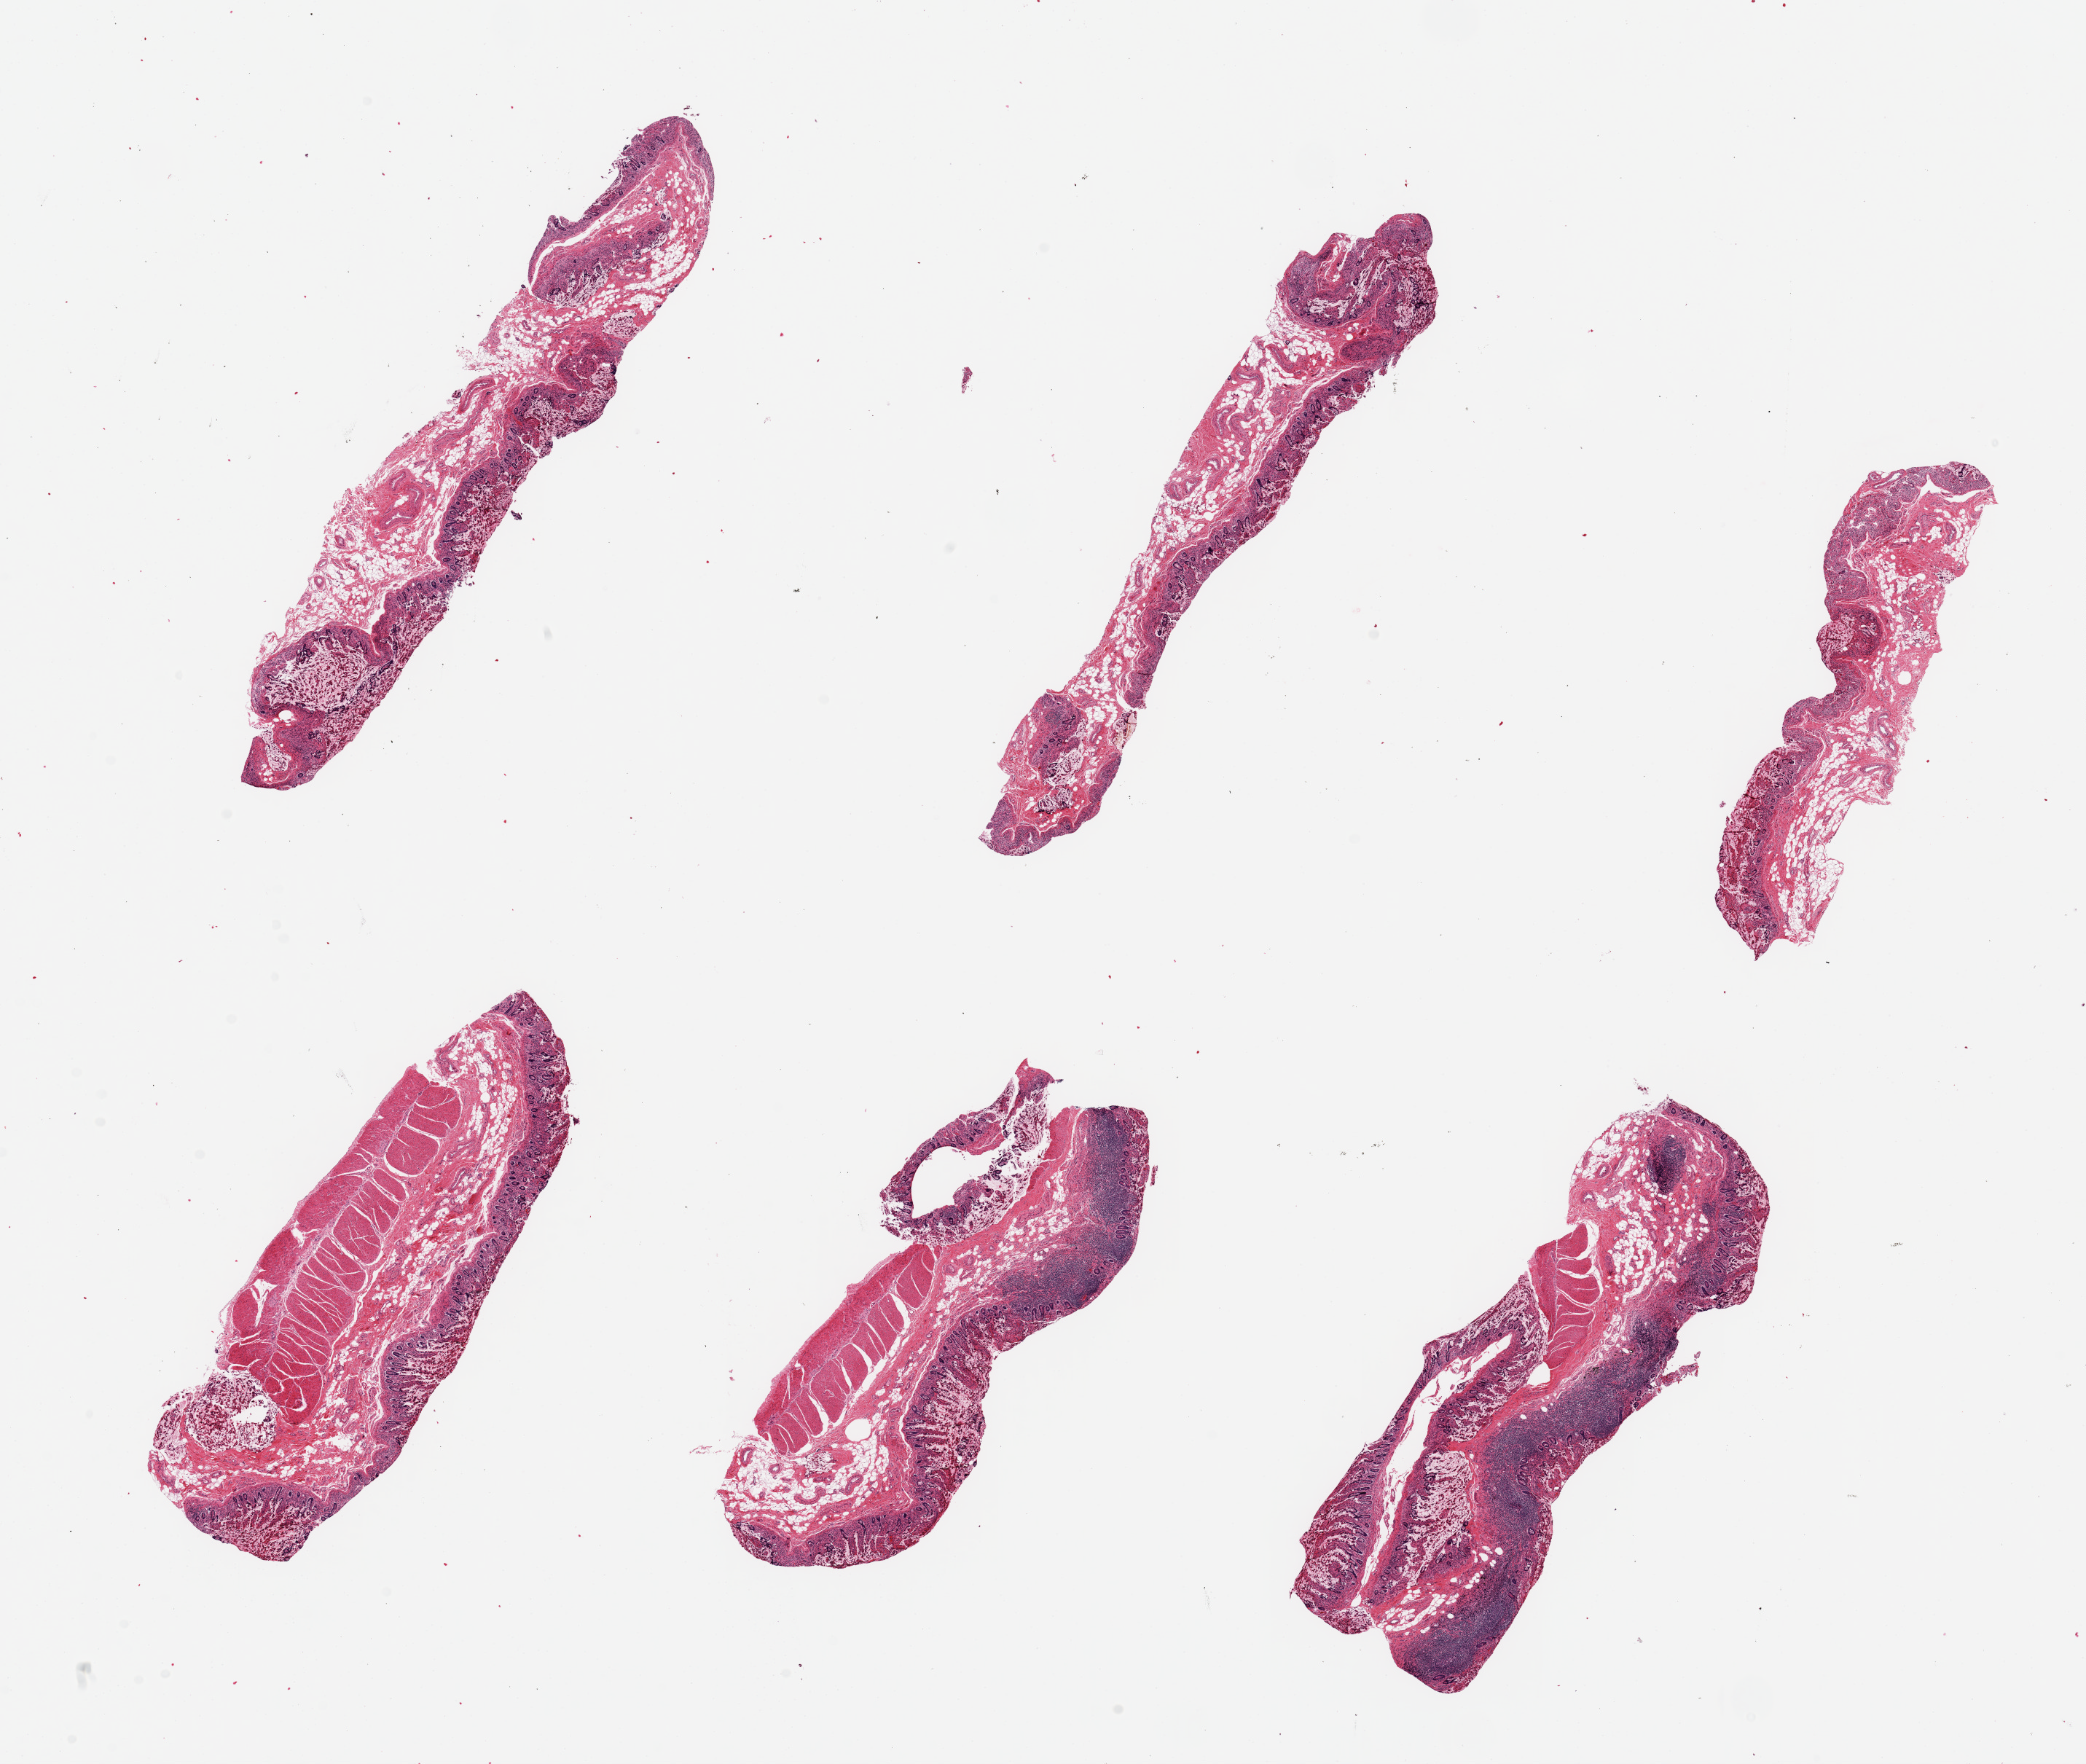
Hematoxylin and eosin (H&E) whole-slide image, brightfield, shown as a low-resolution overview of the whole scanned area (about 22.6 x 19.1 mm, slide scanned at 20x), PAXgene-fixed paraffin-embedded (PFPE) section, sampled site (target tissue): ileum, tissue donor sample. Male donor.
• review note (as recorded): 6 pieces ~7x1mm; Lymphoid elements weel seen in half